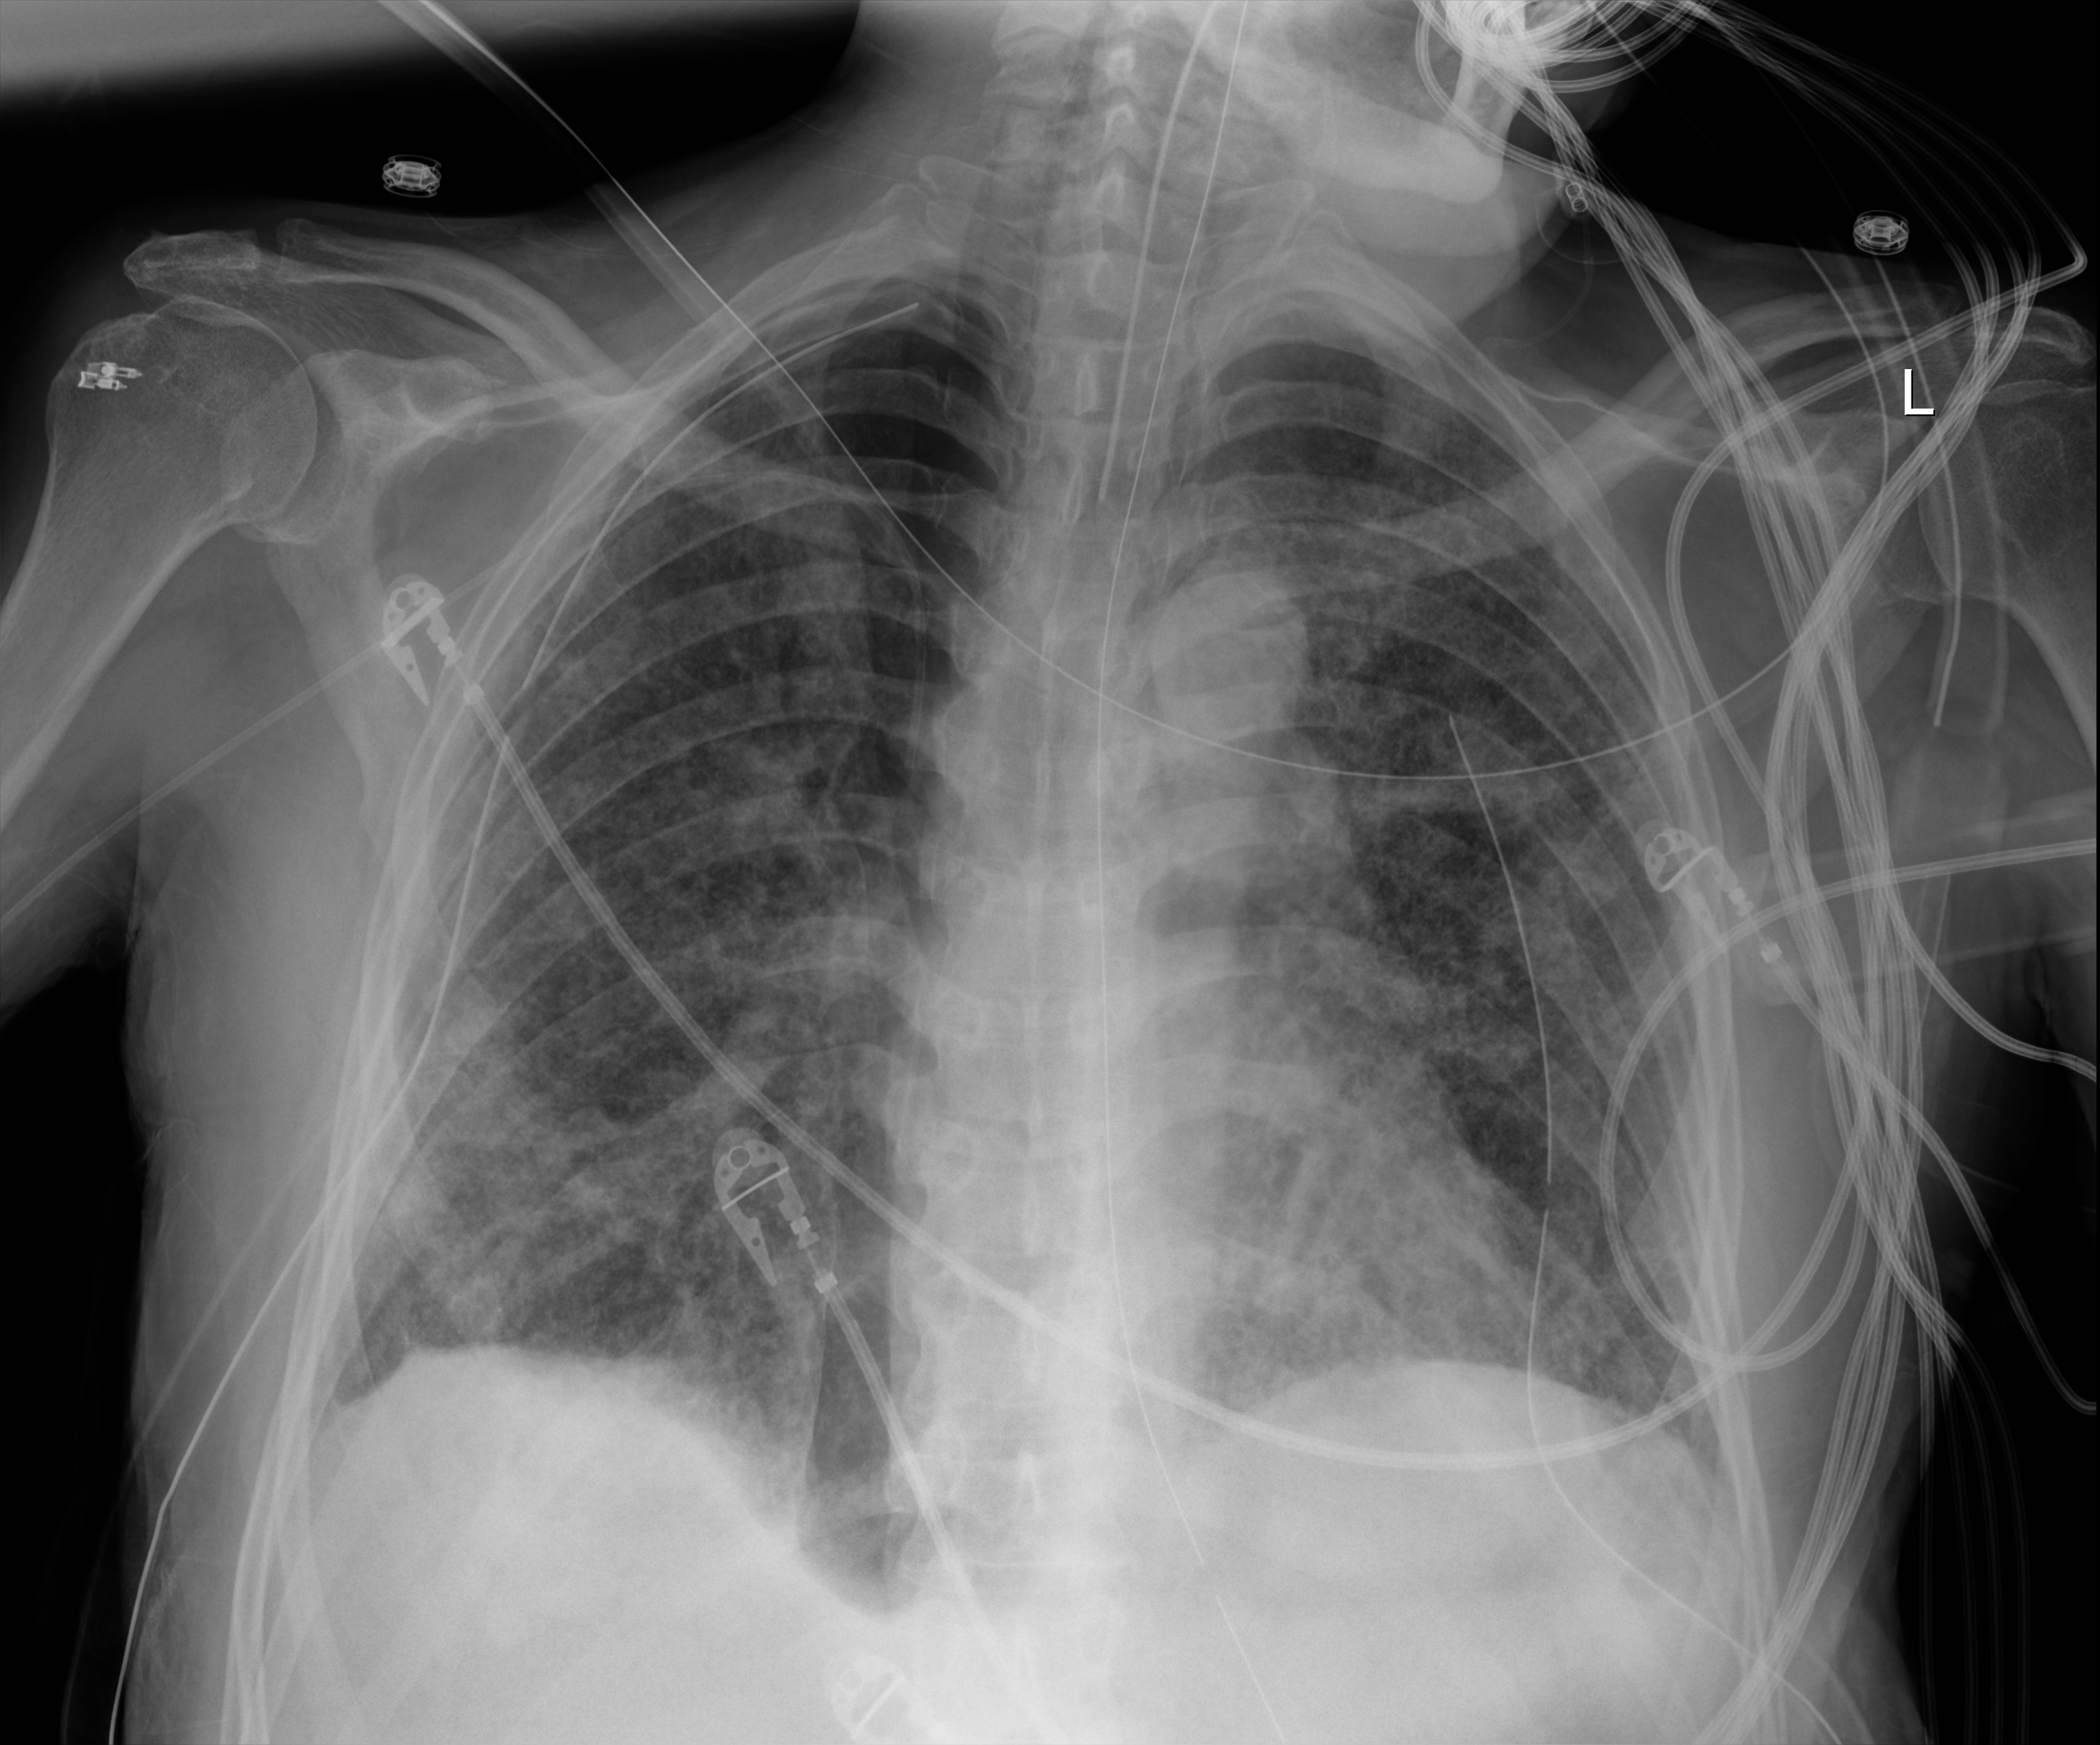
Bedside chest radiograph (digital radiography), anteroposterior (AP) projection. Male patient hospitalised with COVID-19, age 60–74 years.
Admission-level facts for this patient (not findings on this image; timing relative to this image not recorded):
- hypertension (admission record): no